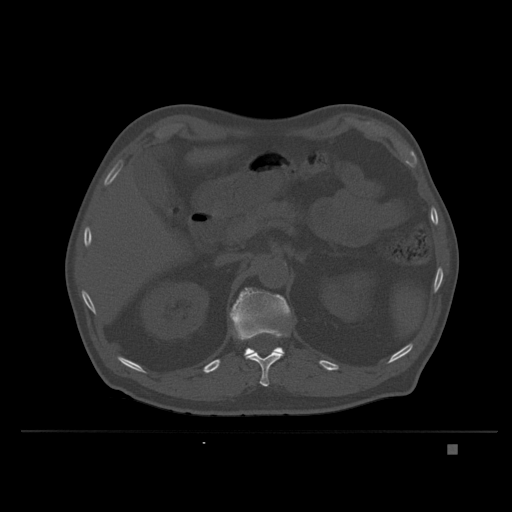
CT including the spine, one axial slice; slice 150 of 435 in the series (ordered by position); bone window (W 1800 / L 400 HU); 1.5 mm slice thickness; 512 × 512 image matrix, field of view 434 × 434 mm. Patient: male, 73 years. Case-level facts recorded for this patient, not image findings: primary cancer: skin.
Structures marked on this image (semi-automatically segmented with operator editing):
- L1 vertebra: bounding box (x1, y1, x2, y2) in pixels: (229, 287, 291, 384)
- T12 vertebra: (247, 351, 283, 387)